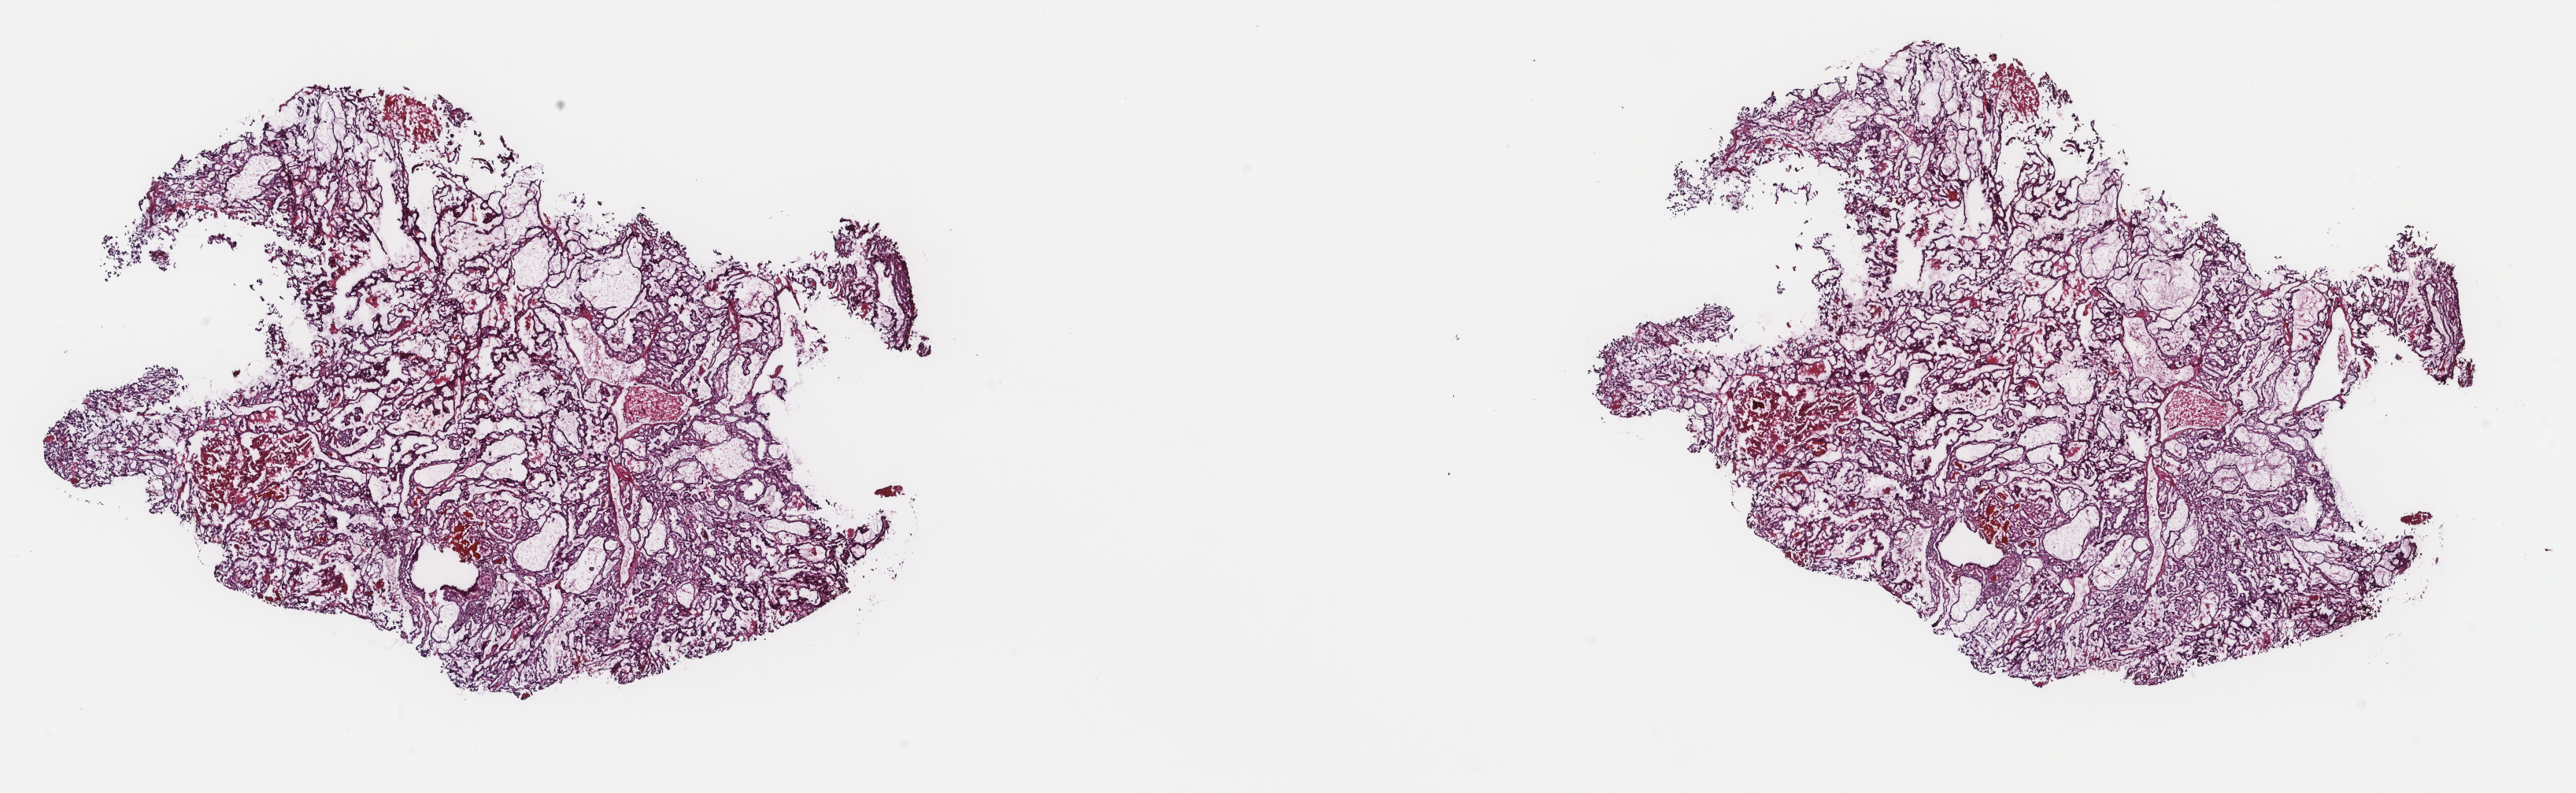
Whole-slide histology image, H&E-stained — low-resolution overview of the scanned area, about 26.0 x 8.0 mm; frozen section from the top of the tissue portion; primary tumour sample from the thyroid. Female, age 36 years at initial diagnosis. Pathologist review of this section (percent, as recorded): tumour cells 100%, tumour nuclei 90%, normal cells 0%, stromal cells 0%, necrosis 0%. Inflammatory infiltration, as recorded: lymphocyte infiltration 0%, monocyte infiltration 0%, neutrophil infiltration 0%.
AJCC pathologic stage: I (6th edition). Pathologic diagnosis: Papillary adenocarcinoma, NOS (thyroid gland). Lymph nodes positive (case pathology): 0 of 1 examined.